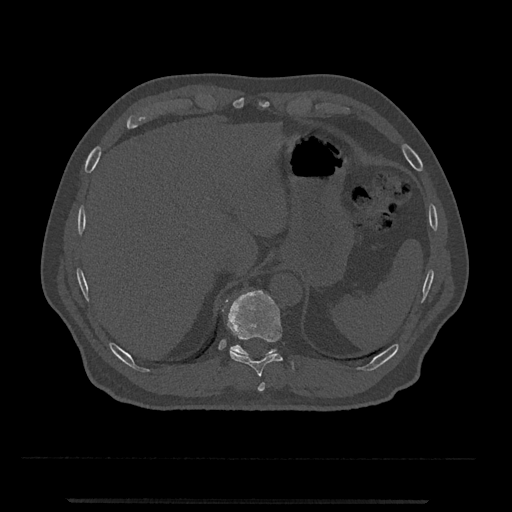
CT including the spine, one axial slice. Position 505 of 797 along the scan axis. Reconstruction kernel Br40s/3. Bone window (W 1800 / L 400 HU). 512 × 512 image matrix, field of view 419 × 419 mm. Patient: male, 63 years. Case-level facts recorded for this patient, not image findings: primary cancer: prostate.
Structures marked on this image (semi-automatic segmentation, software-assisted and operator-edited):
- T10 vertebra: box from (x=222, y=290) to (x=294, y=377) px
- T11 vertebra: (x=230, y=345)–(x=277, y=357)
- T9 vertebra: (x=258, y=382)–(x=265, y=392)